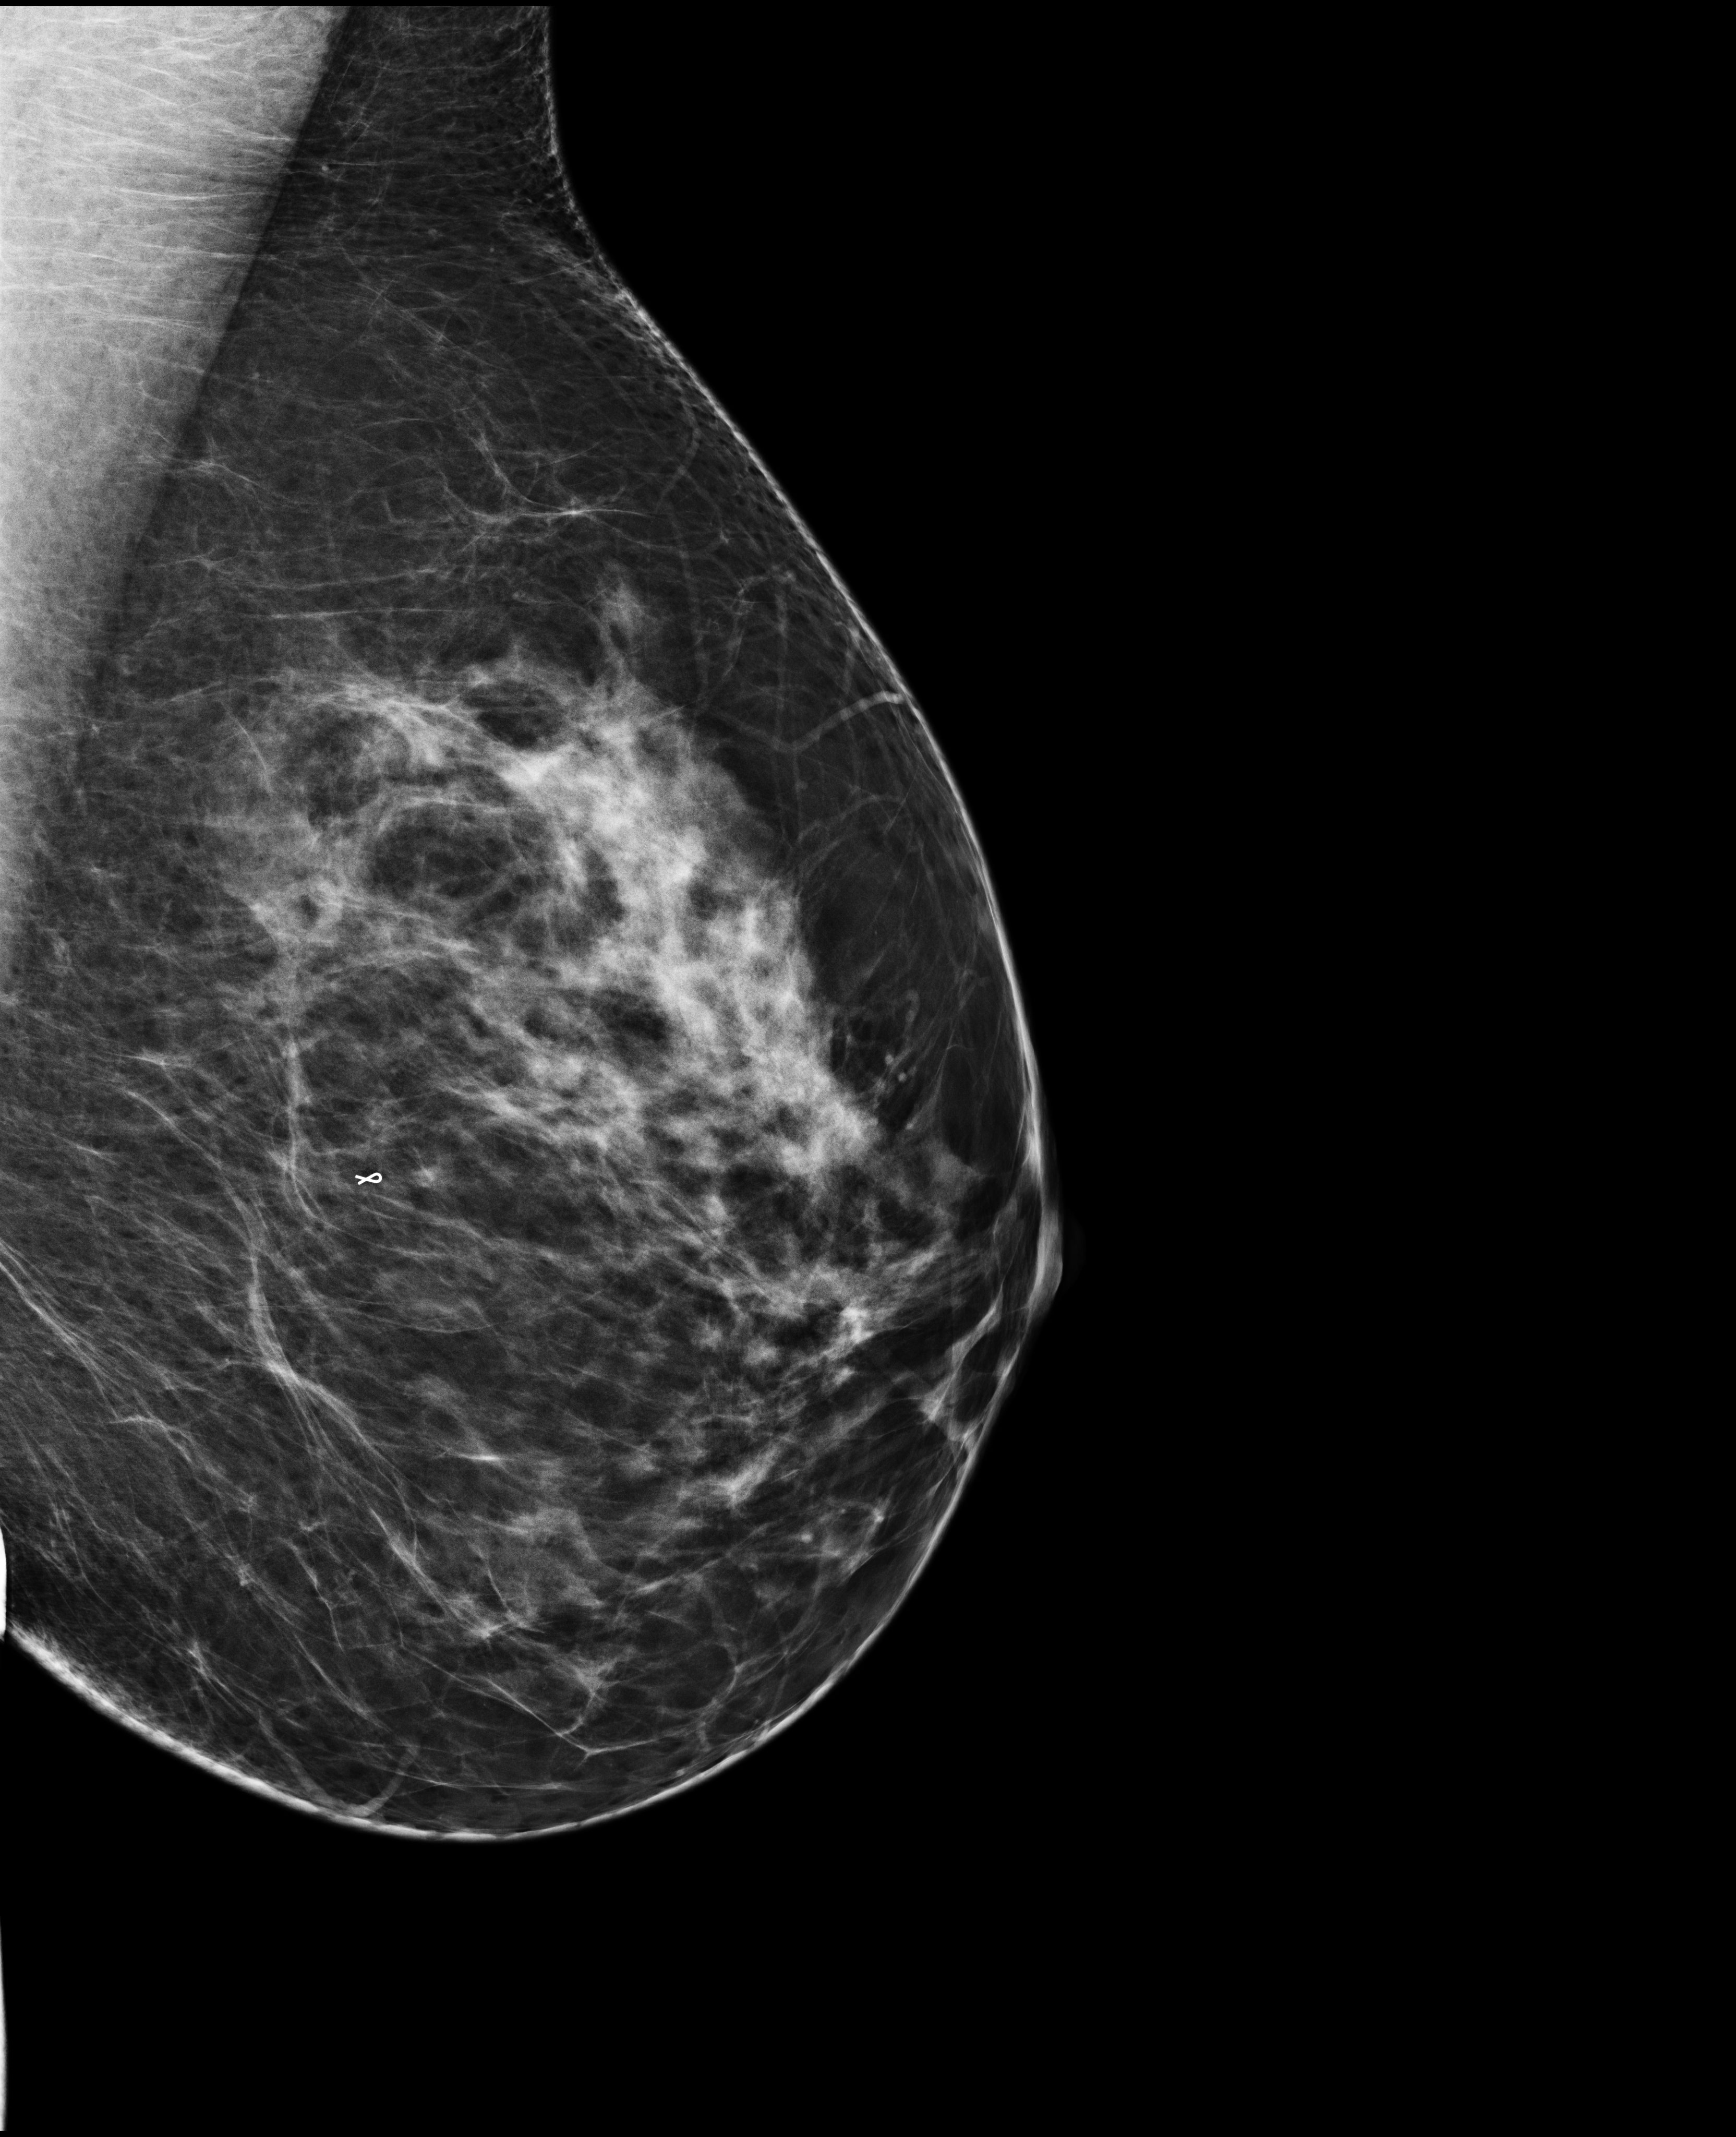
Digital mammogram (FFDM); left breast; medio-lateral oblique projection; annual screening mammography examination; compressed breast thickness 85 mm; system: Selenia Dimensions. Female patient, age 50 years.
Breast density at the screening exam (both breasts): heterogeneously dense (BI-RADS density category c). Final BI-RADS assessment for this screening round (tomosynthesis exam, both breasts): category 1. Recall: no recall after this screen.